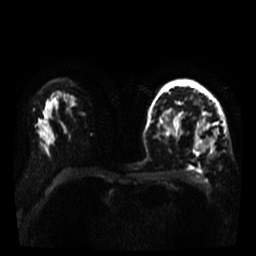
Breast MRI, one axial slice. Slice 22 of 35 in the series (ordered by position). Diffusion-weighted series; image 2 of 4 stored at this slice position (different b-values; order by instance number). 3 T. 256 × 256 image matrix, field of view 320 × 320 mm. Female patient.
Outlined on this slice (outlined manually by an expert reader):
- tumour on diffusion-weighted imaging: bounding box (x1, y1, x2, y2) in pixels: (194, 126, 216, 154)